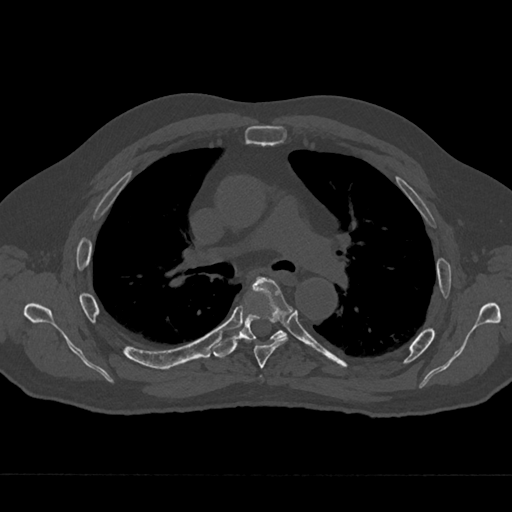
CT including the spine, one axial slice; slice 452 of 797 in the series (ordered by position); reconstruction kernel Br40s/3; 120 kVp; bone window (W 1800 / L 400 HU); 512 × 512 image matrix. Male patient, age 75 years. From the clinical record (not read from this slice): primary cancer: renal.
Outlined on this slice (semi-automatic segmentation, software-assisted and operator-edited):
- T4 vertebra: box from (x=260, y=375) to (x=262, y=377) px
- T5 vertebra: (x=252, y=277)–(x=292, y=368)
- T6 vertebra: (x=213, y=277)–(x=287, y=358)